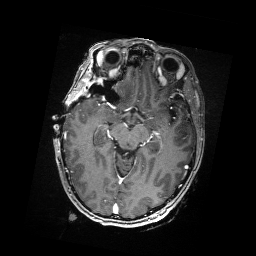
Brain MRI from a brain-tumour surgery series, one axial slice; position 104 of 176 along the scan axis; T1-weighted post-contrast; 1 mm slice thickness; 256 × 256 image matrix, field of view 256 × 256 mm. From the clinical record (not read from this slice): histopathology: Metastatic Carcinoma from Breast primary; tumour location: Right Frontal.
Structures marked on this image (outlined manually by an expert reader):
- residual tumour: box from (x=99, y=90) to (x=104, y=95) px